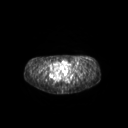
FDG PET of an extremity soft-tissue mass (from a PET/CT study), one axial slice. Position 78 of 267 along the scan axis. 3.27 mm slice thickness. 128 × 128 image matrix. Female patient, age 24 years. Case-level facts recorded for this patient, not image findings: histological type: leiomyosarcoma; grade: high; site of the primary tumour: groin.
Structures marked on this image (expert contour drawn on MRI and transferred to this co-registered scan by the dataset authors):
- gross tumour volume including surrounding oedema: bounding box (x1, y1, x2, y2) in pixels: (77, 58, 92, 64)
- gross tumour volume (mass): (78, 61, 83, 64)